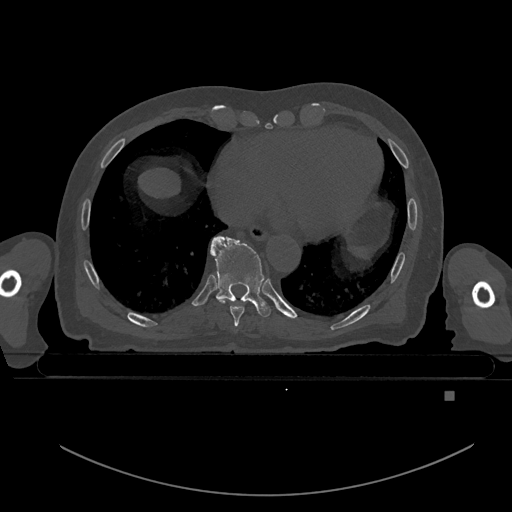
CT including the spine, one axial slice. Slice 167 of 969 in the series (ordered by position). Bone window (W 1800 / L 400 HU). 0.5 mm slice thickness. 512 × 512 image matrix, field of view 456 × 456 mm. Patient: male, 82 years. From the clinical record (not read from this slice): primary cancer: prostate.
Annotated regions visible in this slice (semi-automatic segmentation, software-assisted and operator-edited):
- T8 vertebra: bounding box (x1, y1, x2, y2) in pixels: (215, 298, 251, 327)
- T9 vertebra: (210, 235, 271, 317)